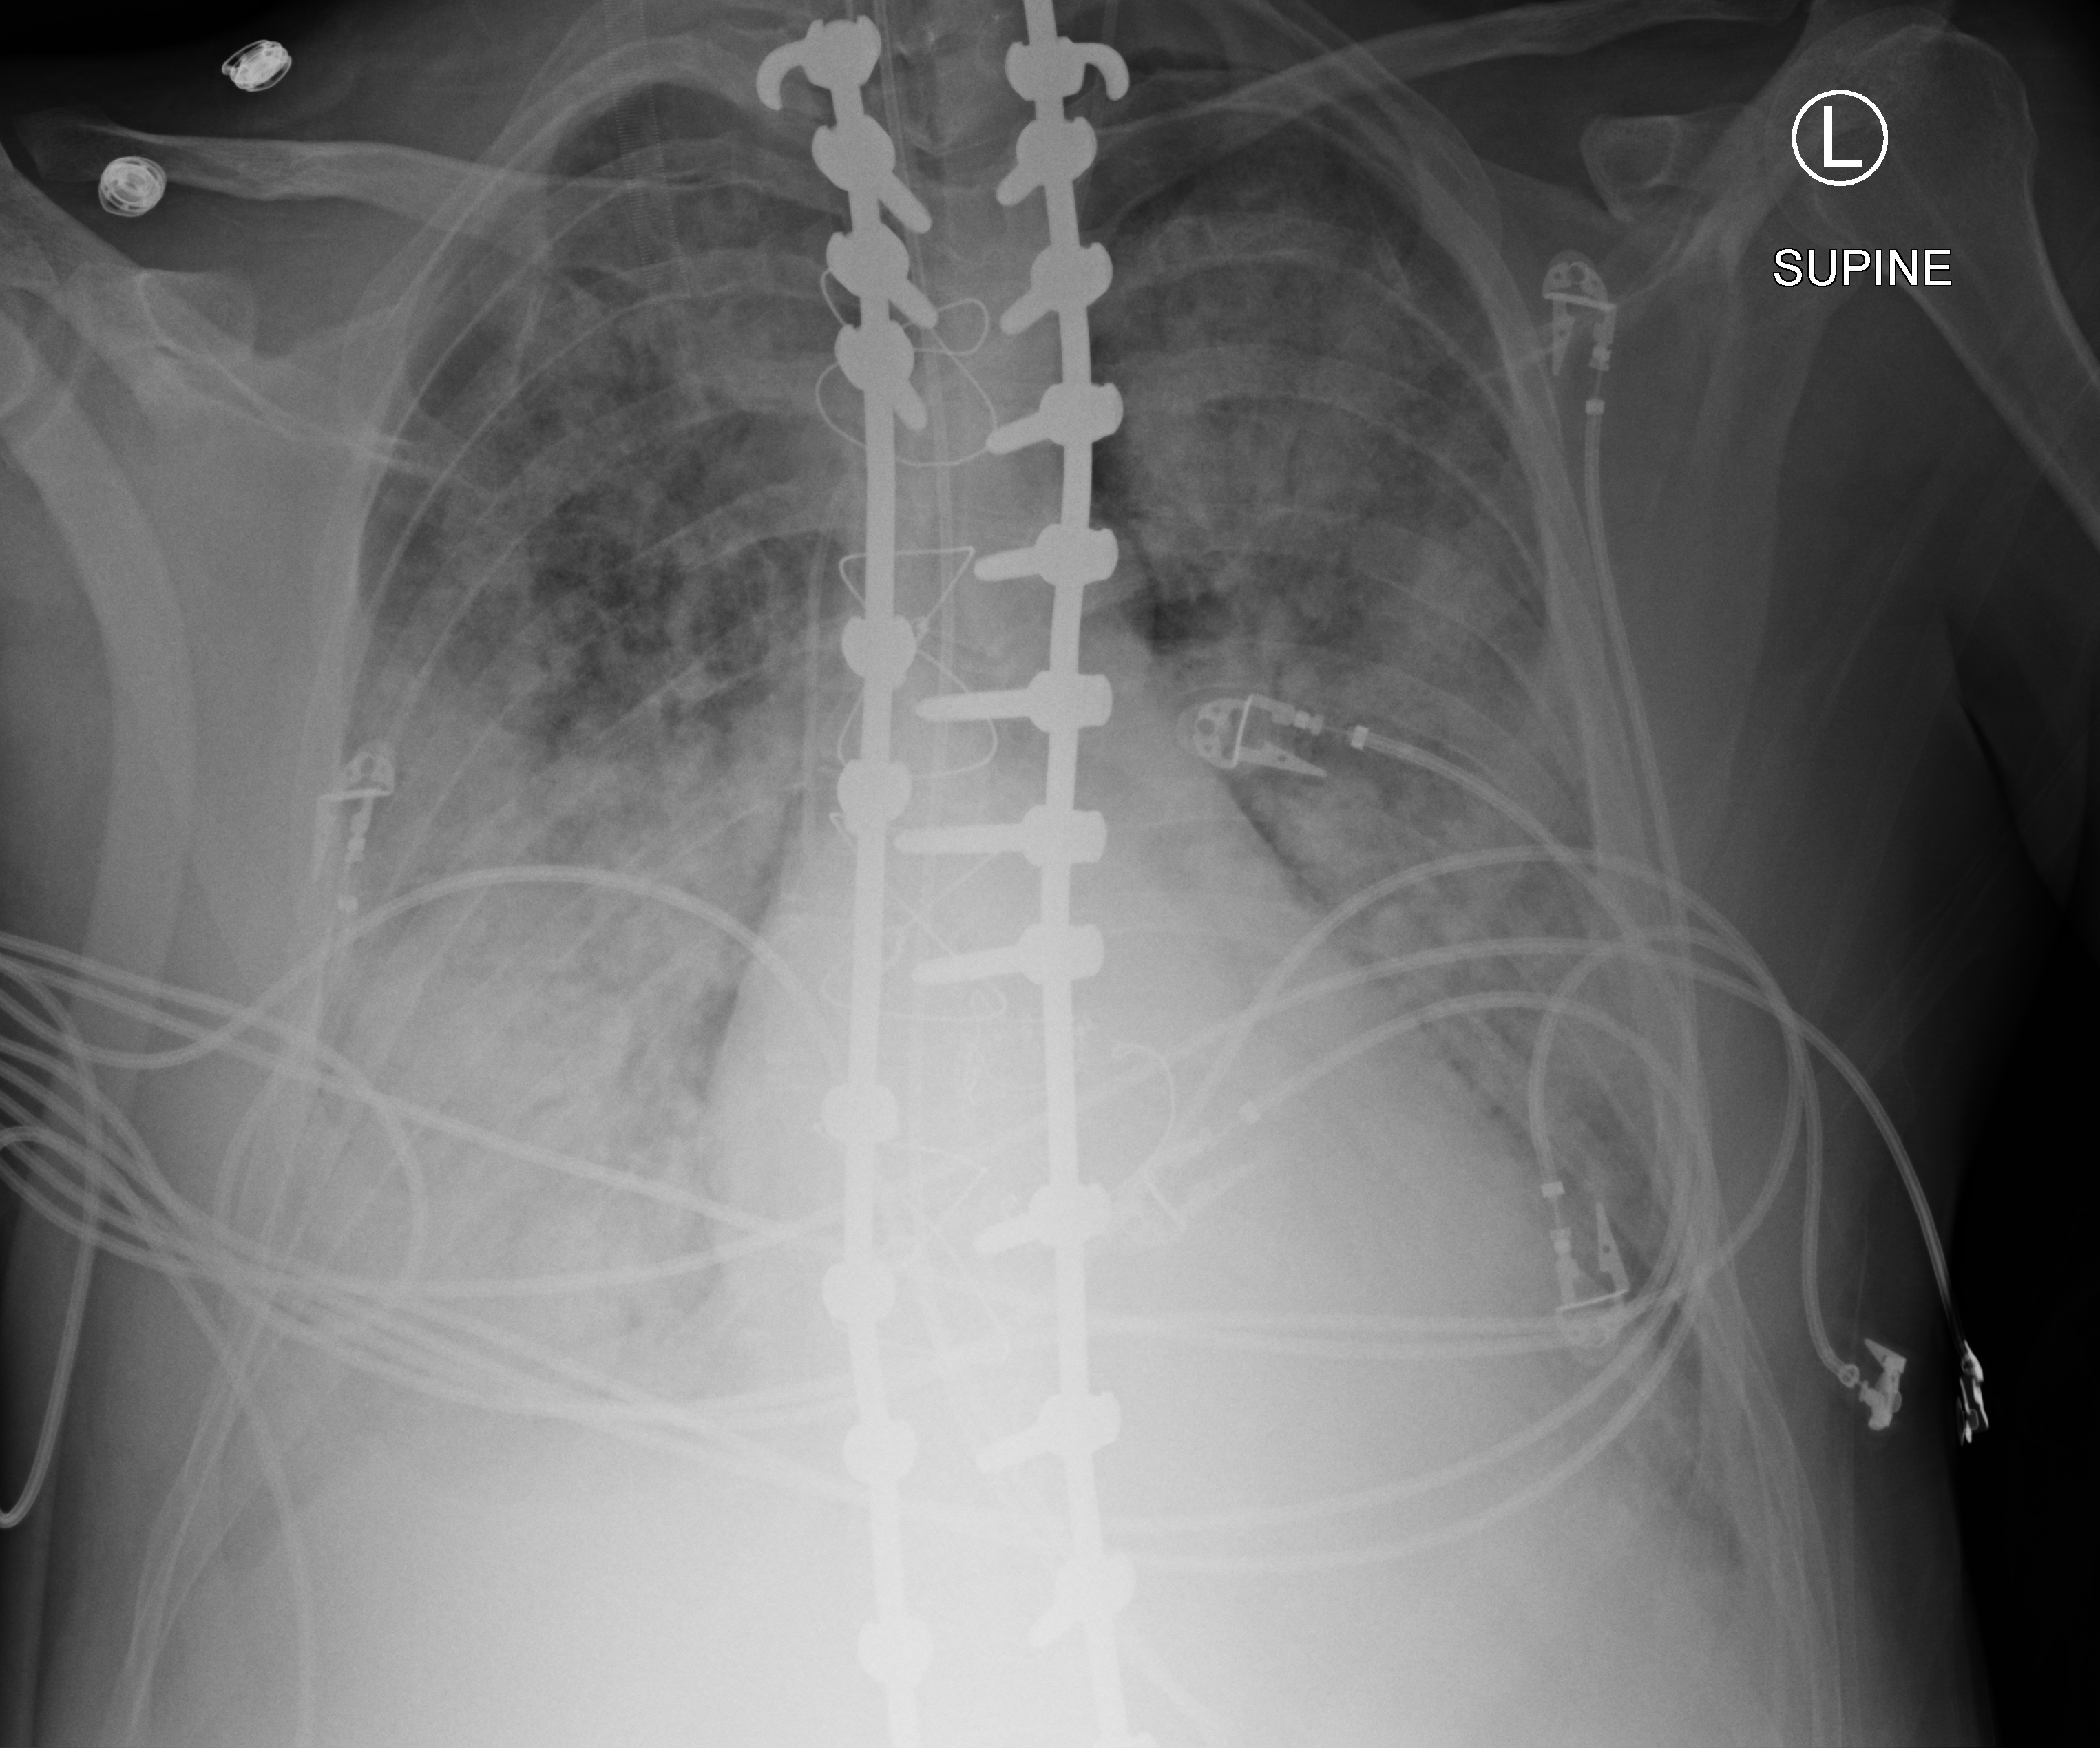
Chest X-ray (portable). Adult patient hospitalised with COVID-19, age 18–59 years.
Admission-level facts for this patient (not findings on this image; timing relative to this image not recorded): length of hospital stay: 15 days; mechanically ventilated during this hospital stay: yes.